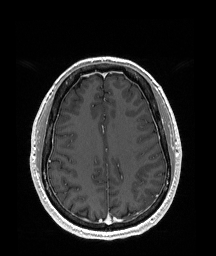
Brain MRI from a brain-tumour surgery series, one axial slice; position 69 of 192 along the scan axis; T1-weighted post-contrast; 1 mm slice thickness; 216 × 256 image matrix. Case-level facts recorded for this patient, not image findings: histopathology: Glioblastoma; WHO grade: 4; IDH mutation: no; tumour location: Left Temporal Parietal.
Structures marked on this image (outlined manually by an expert reader):
- tumour: box from (x=145, y=190) to (x=156, y=202) px